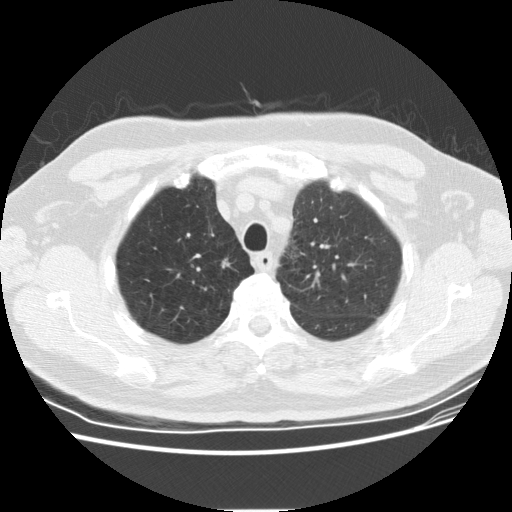
Axial slice from a low-dose chest CT screening exam, second annual screen, lung window (W 1500 / L -600 HU), 2.5 mm slice thickness, standard (soft-tissue) reconstruction kernel (STANDARD). Male participant, aged 69 years at enrolment.
- Lesion marked by an expert reader, bounding box [x1, y1, x2, y2] px = [210, 253, 241, 282].
- Screening reader's record for this exam (one nodule recorded; not confirmed to be the boxed lesion): non-calcified nodule or mass ≥4 mm, right lower lobe, 4 × 4 mm, smooth margins, soft tissue attenuation, pre-existing on the prior screen: yes; interval growth: no.
- Official screen result: positive, change unspecified: nodule(s) >= 4 mm or enlarging nodule(s), mass(es), or other non-specific abnormalities suspicious for lung cancer.
- Later outcome: lung cancer diagnosed 435 days after this screen — squamous cell carcinoma, NOS, right upper lobe, moderately differentiated (G2), stage IA (AJCC 6th edition), 9 mm at pathology.